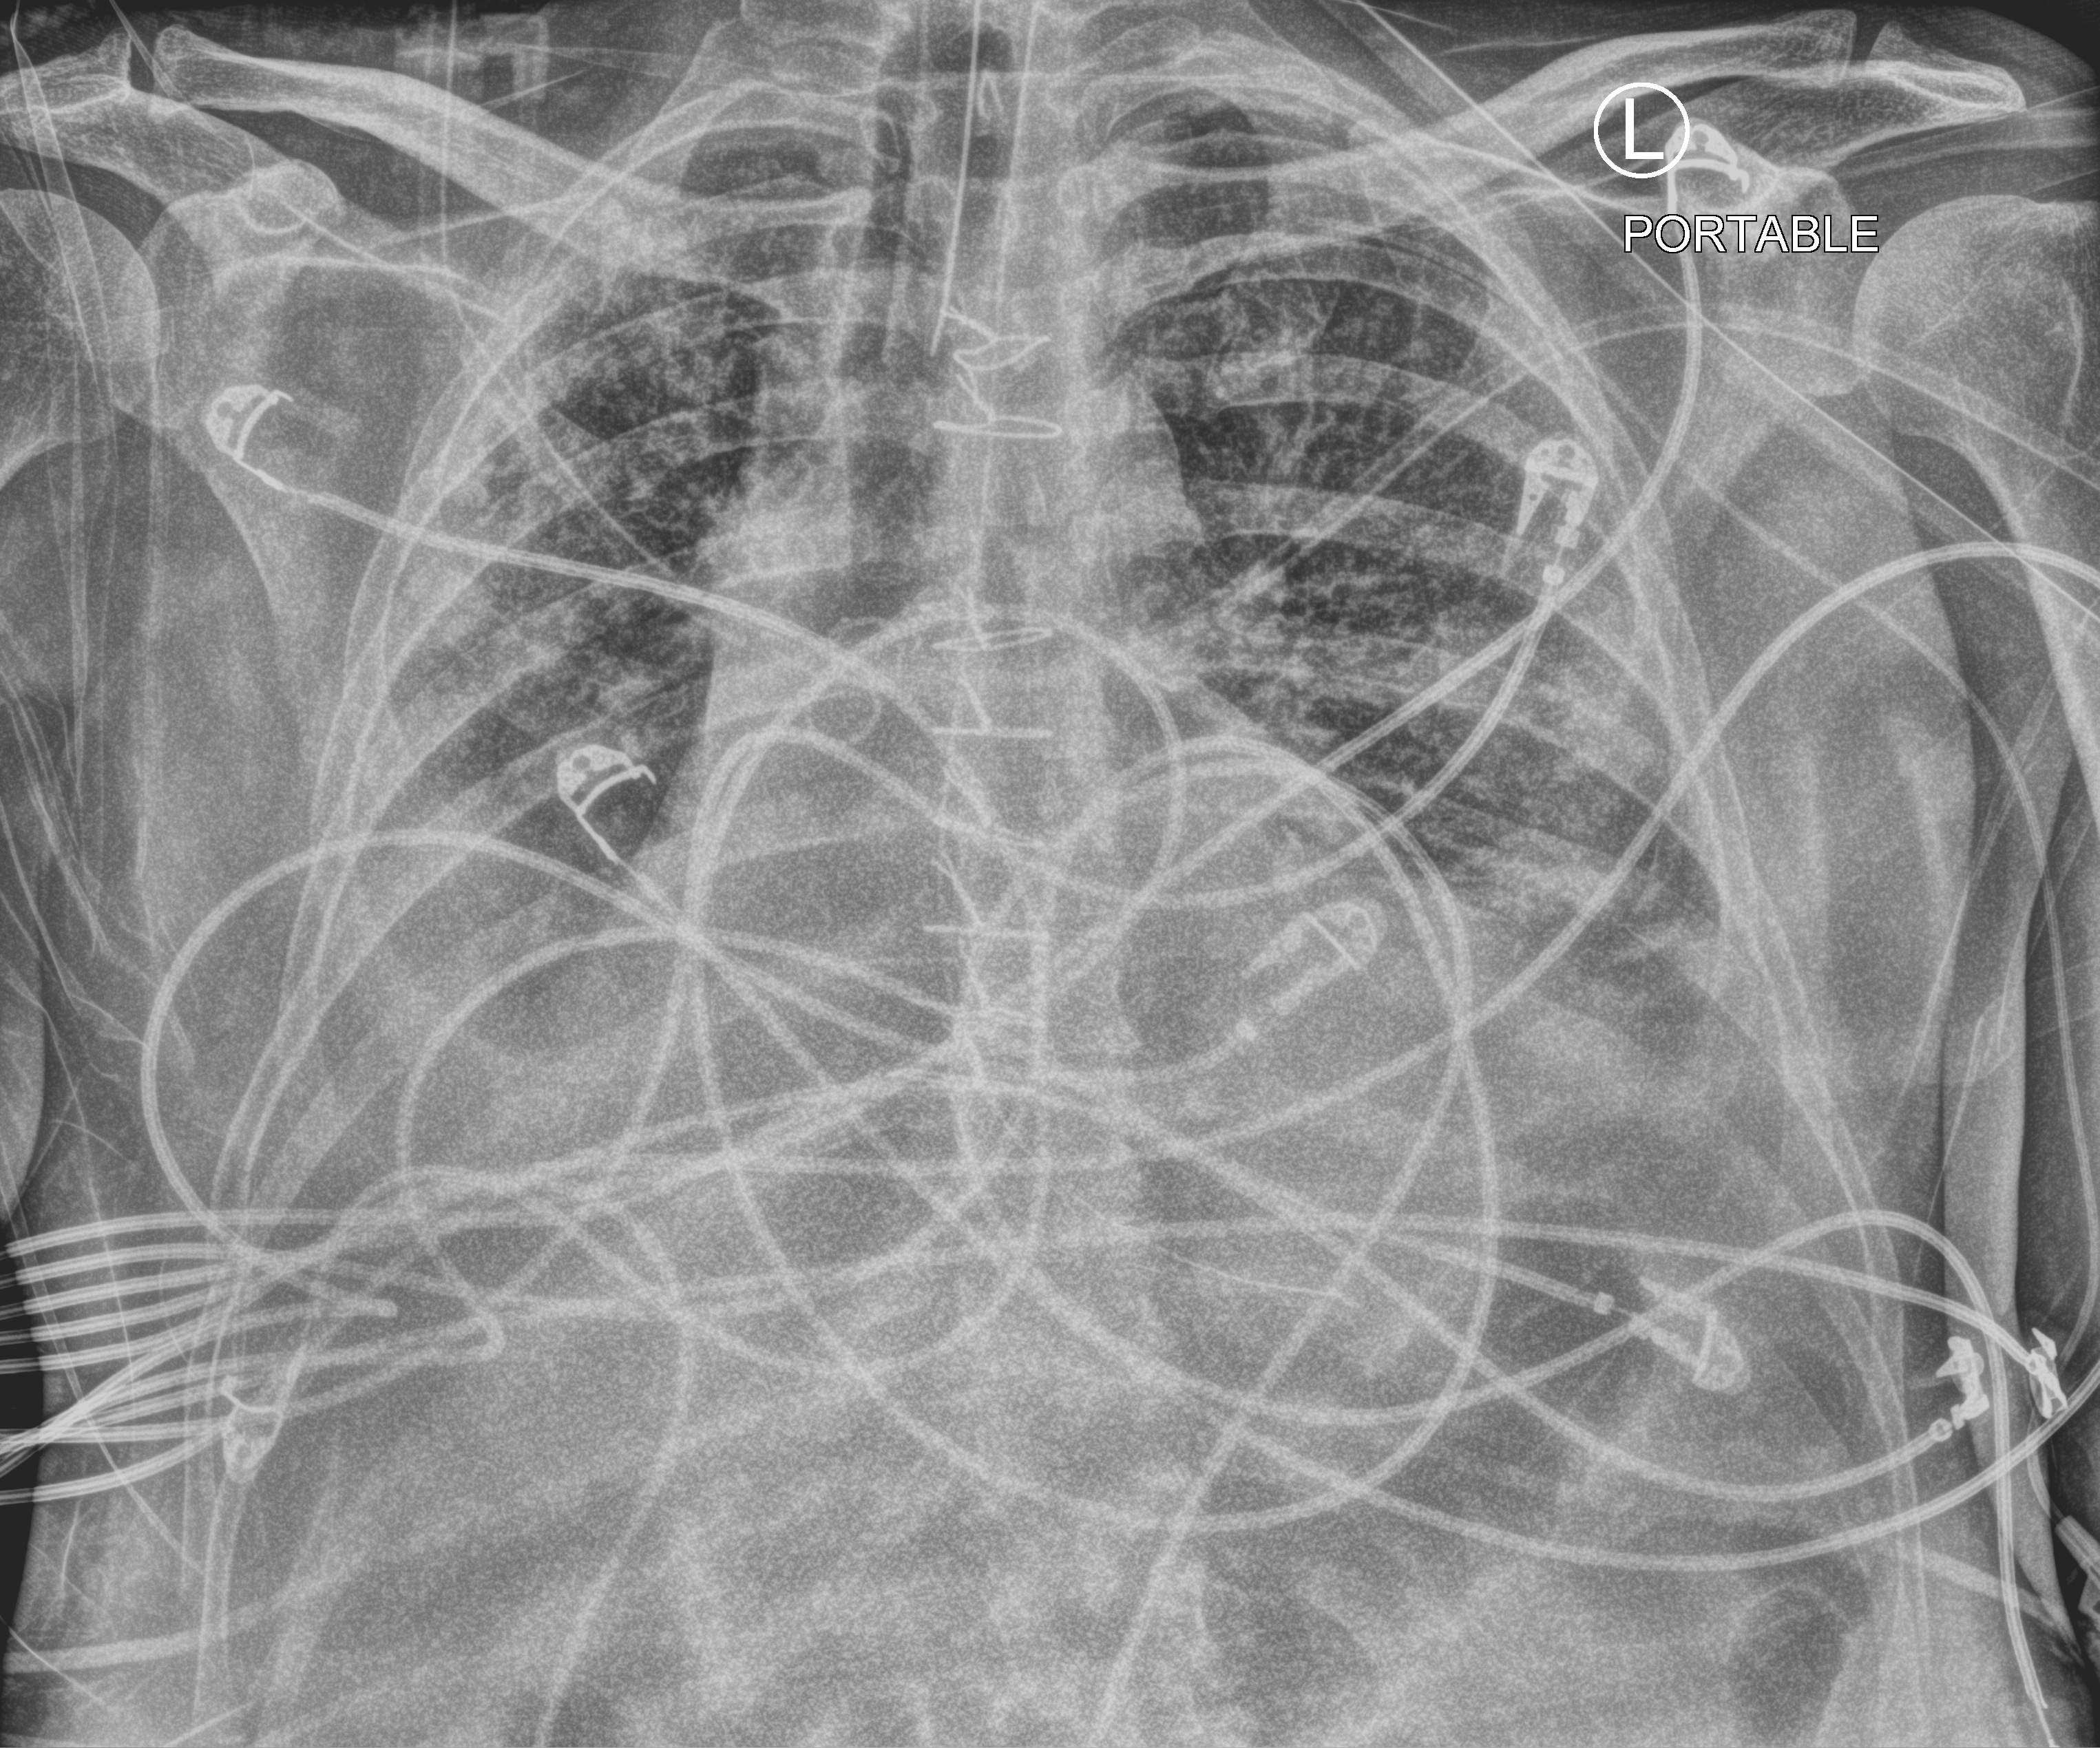
Chest X-ray (portable); anteroposterior (AP) projection. Patient hospitalised with COVID-19; male, aged 18–59 years.
Hospital-stay facts (about this admission, not read from this image; timing relative to this image not recorded): admitted to intensive care during this hospital stay: yes.